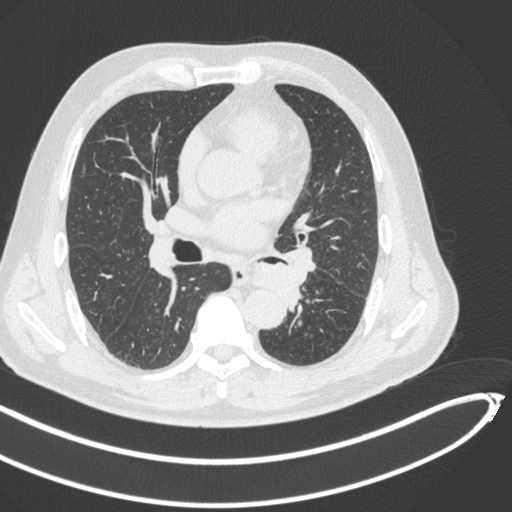
Chest CT, one axial slice. Slice 251 of 466 in the series (ordered by position). Reconstruction kernel B31f. 120 kVp. Lung window (W 1500 / L -600 HU). 512 × 512 image matrix, field of view 400 × 400 mm. Male patient, age 64 years. Case-level facts recorded for this patient, not image findings: clinical TNM (as recorded): T1c N0 M0; histopathological grade: G2.
Outlined on this slice (bounding box drawn by a radiologist):
- lung tumour (recorded histology: squamous cell carcinoma): bounding box [x1, y1, x2, y2] px = [251, 262, 305, 310]